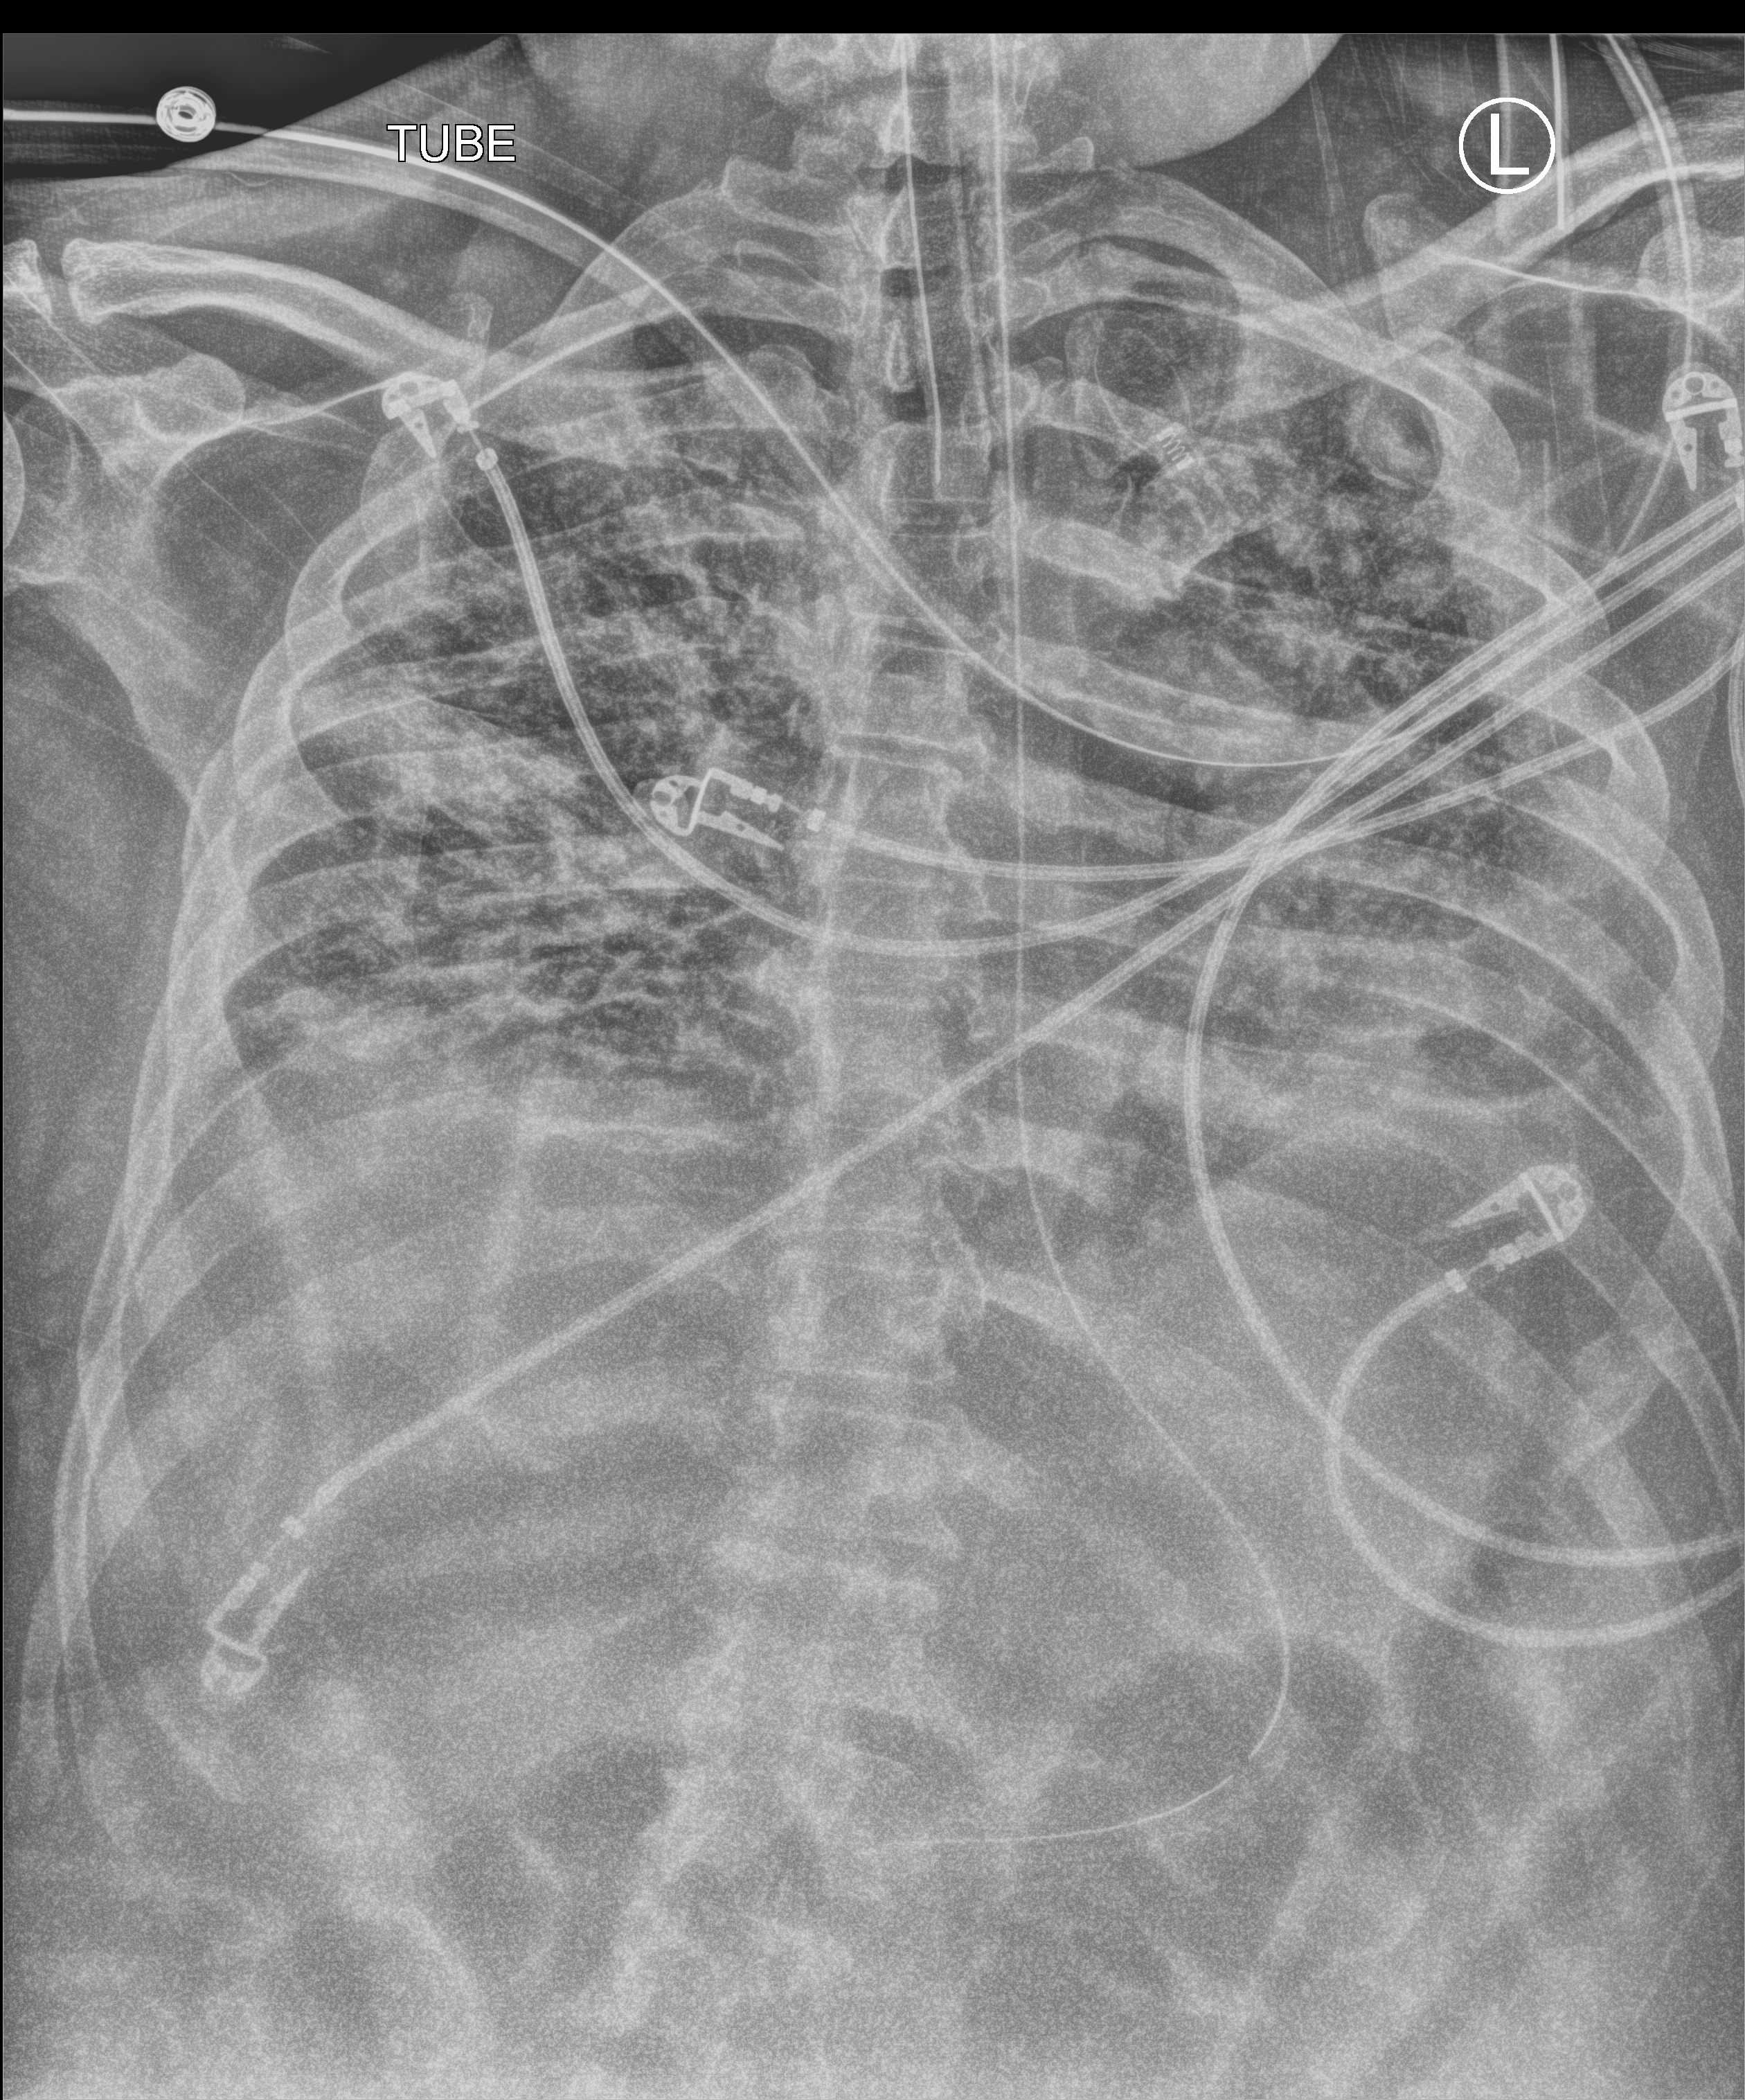
Portable chest radiograph; anteroposterior (AP) projection. Patient hospitalised with COVID-19; male, aged 18–59 years.
From the hospital-stay record, not from the radiograph (when in the stay this image was taken is not recorded): smoking status (admission record): never; admitted to intensive care during this hospital stay: yes; COPD (admission record): no.